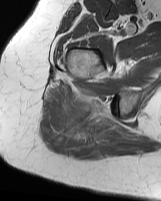
MRI of an extremity soft-tissue mass, one axial slice. Slice 46 of 70 in the series (ordered by position). MR volume resampled by the dataset authors to the PET/CT grid (not the native acquisition matrix). 161 × 201 image matrix, field of view 157 × 196 mm. Female patient. Case-level facts recorded for this patient, not image findings: histological type: synovial sarcoma; grade: intermediate; site of the primary tumour: right buttock.
Structures marked on this image (expert contour drawn on MRI and transferred to this co-registered scan by the dataset authors):
- gross tumour volume including surrounding oedema: box from (x=56, y=93) to (x=125, y=148) px
- gross tumour volume (mass): (x=67, y=93)–(x=96, y=114)